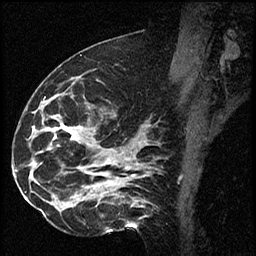
Breast MRI (dynamic contrast-enhanced), one sagittal slice. Dynamic contrast-enhanced series, image 2 of 2 at this slice position (ordered by acquisition). 1.5 T. TE 4.2 ms, TR 17.3 ms. 2 mm slice thickness. 256 × 256 image matrix, field of view 200 × 200 mm. Female patient. From the clinical record (not read from this slice): setting: breast cancer imaged before/during neoadjuvant chemotherapy; receptor status: HR-positive, HER2-negative.
Outlined on this slice (semi-automatically segmented with operator editing):
- analysis volume of interest (the breast-tissue region the enhancement analysis was run in; not a lesion): bounding box (x1, y1, x2, y2) in pixels: (41, 94, 115, 223)
- tumour enhancement mask (voxels above the 100 % enhancement threshold inside the analysis volume of interest): (69, 129, 77, 139)